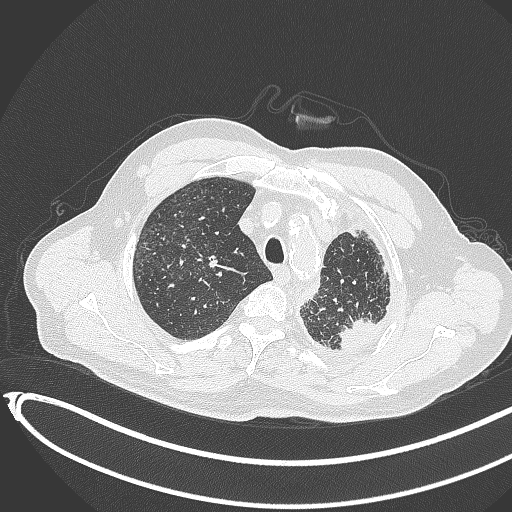
Chest CT, one axial slice. Position 354 of 451 along the scan axis. 120 kVp. Lung window (W 1500 / L -600 HU). 512 × 512 image matrix, field of view 400 × 400 mm. Patient: male, 78 years. From the clinical record (not read from this slice): clinical TNM (as recorded): T1c N0 M1.
Outlined on this slice (bounding box drawn by a radiologist):
- lung tumour (recorded histology: adenocarcinoma): box from (x=332, y=314) to (x=380, y=360) px